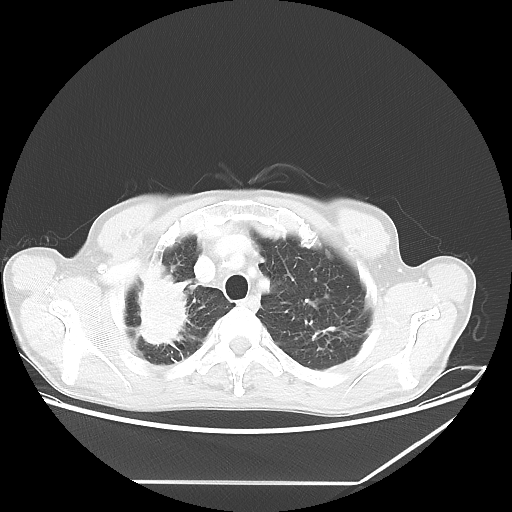
Chest CT, one axial slice. Reconstruction kernel LUNG. 80 kVp. Lung window (W 1500 / L -600 HU). 5 mm slice thickness. 512 × 512 image matrix, field of view 397 × 397 mm. Male patient, age 68 years. Case-level facts recorded for this patient, not image findings: clinical TNM (as recorded): T3 N3 M0.
Structures marked on this image (bounding box drawn by a radiologist):
- lung tumour (recorded histology: adenocarcinoma): bounding box (x1, y1, x2, y2) in pixels: (122, 254, 194, 359)